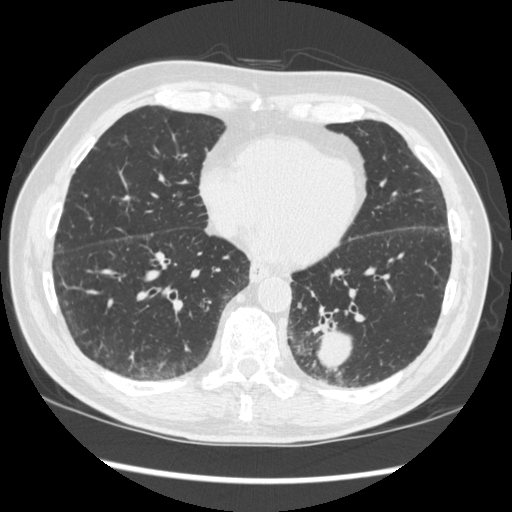
Axial slice from a low-dose chest CT screening exam, baseline annual screen, lung window (W 1500 / L -600 HU), slice 117 of 348 in the series. Male, age 72 years at enrolment. Current smoker at enrolment.
Expert reader's lesion annotation, bounding box <274,295,378,383> (left, top, right, bottom; pixels). The screening reader recorded 2 non-calcified nodules or masses ≥4 mm on this exam; which of them this box marks is not recorded. Official screen result: positive, change unspecified: nodule(s) >= 4 mm or enlarging nodule(s), mass(es), or other non-specific abnormalities suspicious for lung cancer. Lung cancer was diagnosed 37 days after this screen: squamous cell carcinoma, NOS, left lower lobe, stage IIIA (AJCC 6th edition), 60 mm at pathology.